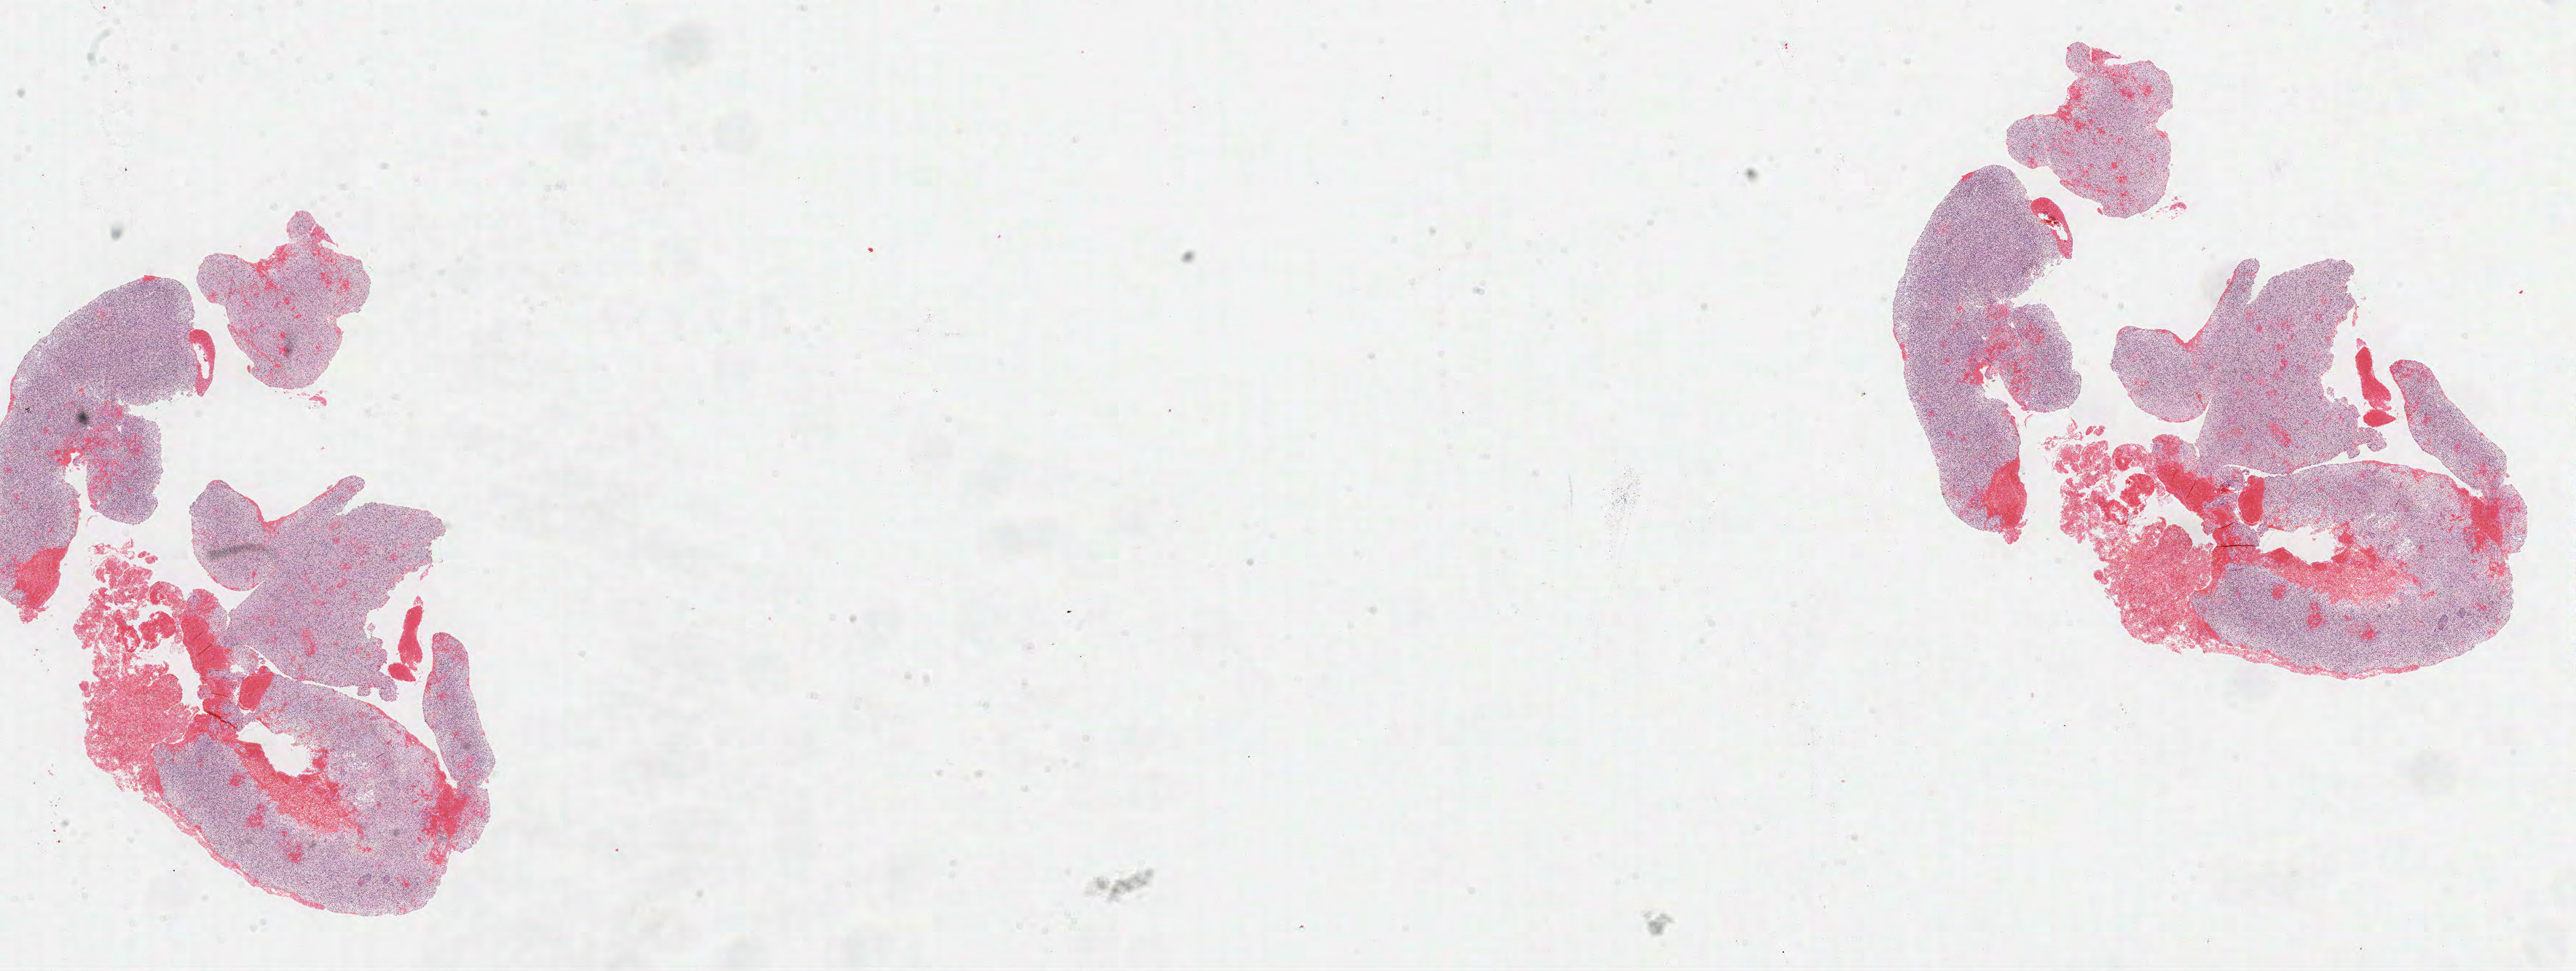
Hematoxylin and eosin (H&E) stained whole-slide image — a low-resolution overview of the entire scanned area, about 28.5 x 10.7 mm (slide scanned at 40x); formalin-fixed paraffin-embedded (FFPE) diagnostic section; brain, primary tumour sample. Male patient; age at initial diagnosis 63 years. Histologic grade: G3 (poorly differentiated).
• pathologic diagnosis: Oligodendroglioma, anaplastic (cerebrum)